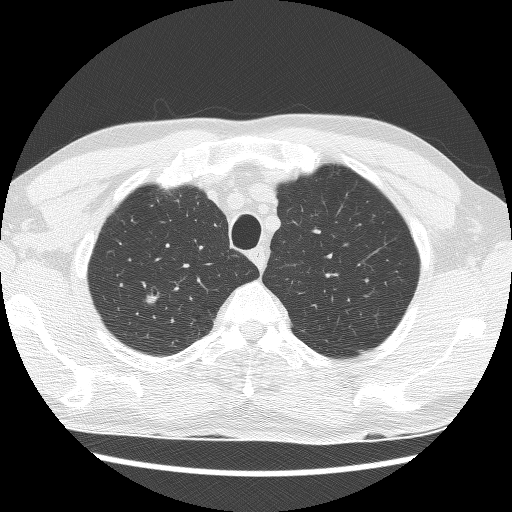
Axial slice from a low-dose chest CT screening exam; second annual screen; lung window (W 1500 / L -600 HU); lung (sharp) reconstruction kernel (BONE); 512 × 512 image matrix. Male, age 66 years at enrolment.
Expert reader's lesion annotation, bounding box [x1, y1, x2, y2] px = [136, 285, 171, 314]. The exam's reader record, not a measurement of the box and not confirmed to be the same lesion: non-calcified nodule or mass ≥4 mm, right upper lobe, 7 × 6 mm, poorly defined margins, mixed attenuation, pre-existing on the prior screen: yes; interval growth: yes. Official screen result: positive, other. Later outcome: lung cancer diagnosed 277 days after this screen — squamous cell carcinoma, NOS, right upper lobe, moderately differentiated (G2), stage IIB (AJCC 6th edition), 39 mm at pathology.